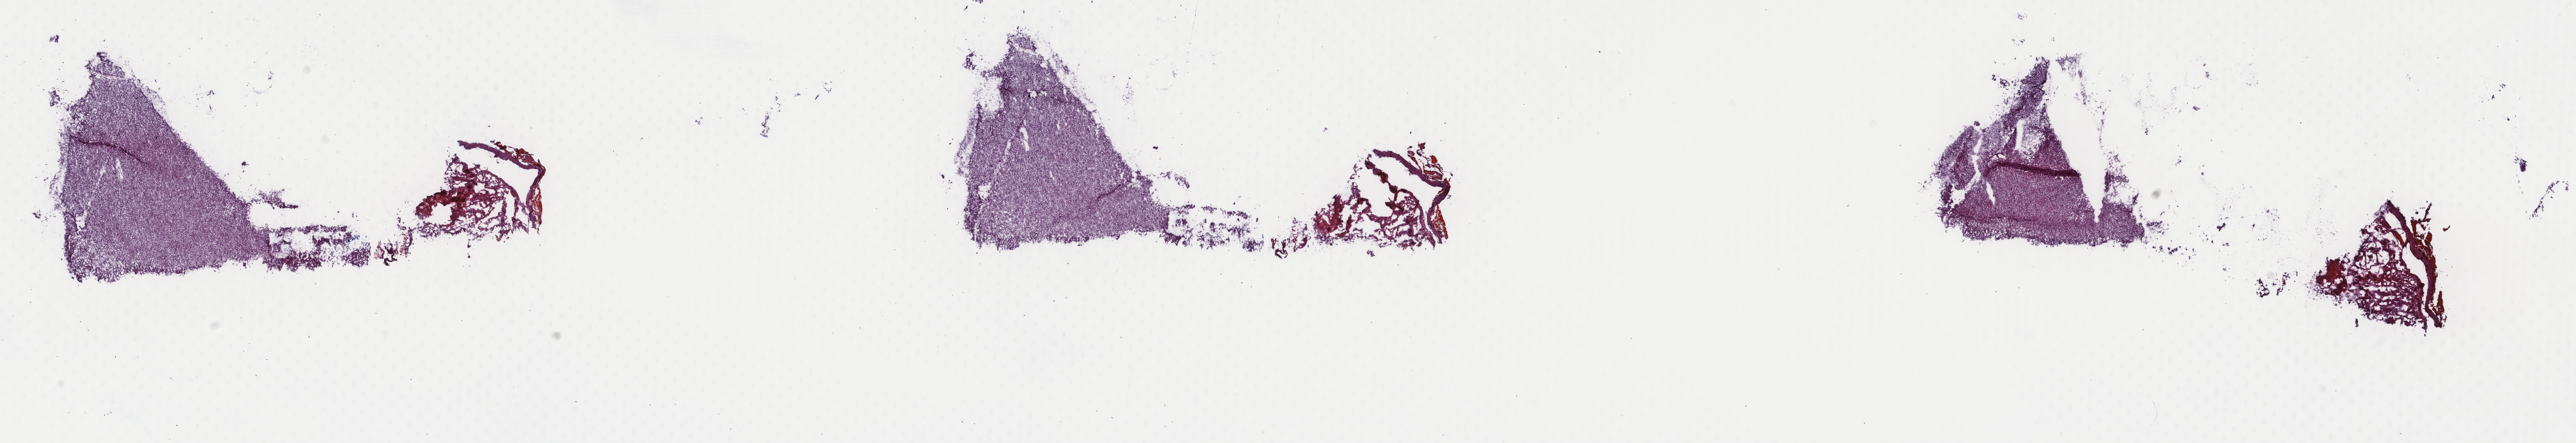
Whole-slide histology image, Hematoxylin and eosin (H&E) stained — a low-resolution overview of the entire scanned area, about 29.3 x 5.0 mm (from a 40x scan); frozen section; brain, primary tumour sample. Female patient; age at initial diagnosis 33 years. Histologic grade: G2 (moderately differentiated). Slide review estimates, as recorded: tumour cells 75%, tumour nuclei 75%, normal cells 25%, stromal cells 0%, necrosis 0%. Inflammatory infiltration, as recorded: lymphocyte infiltration 0%, monocyte infiltration 0%, neutrophil infiltration 0%.
• pathologic diagnosis: Oligodendroglioma, NOS (cerebrum)
• laterality: right